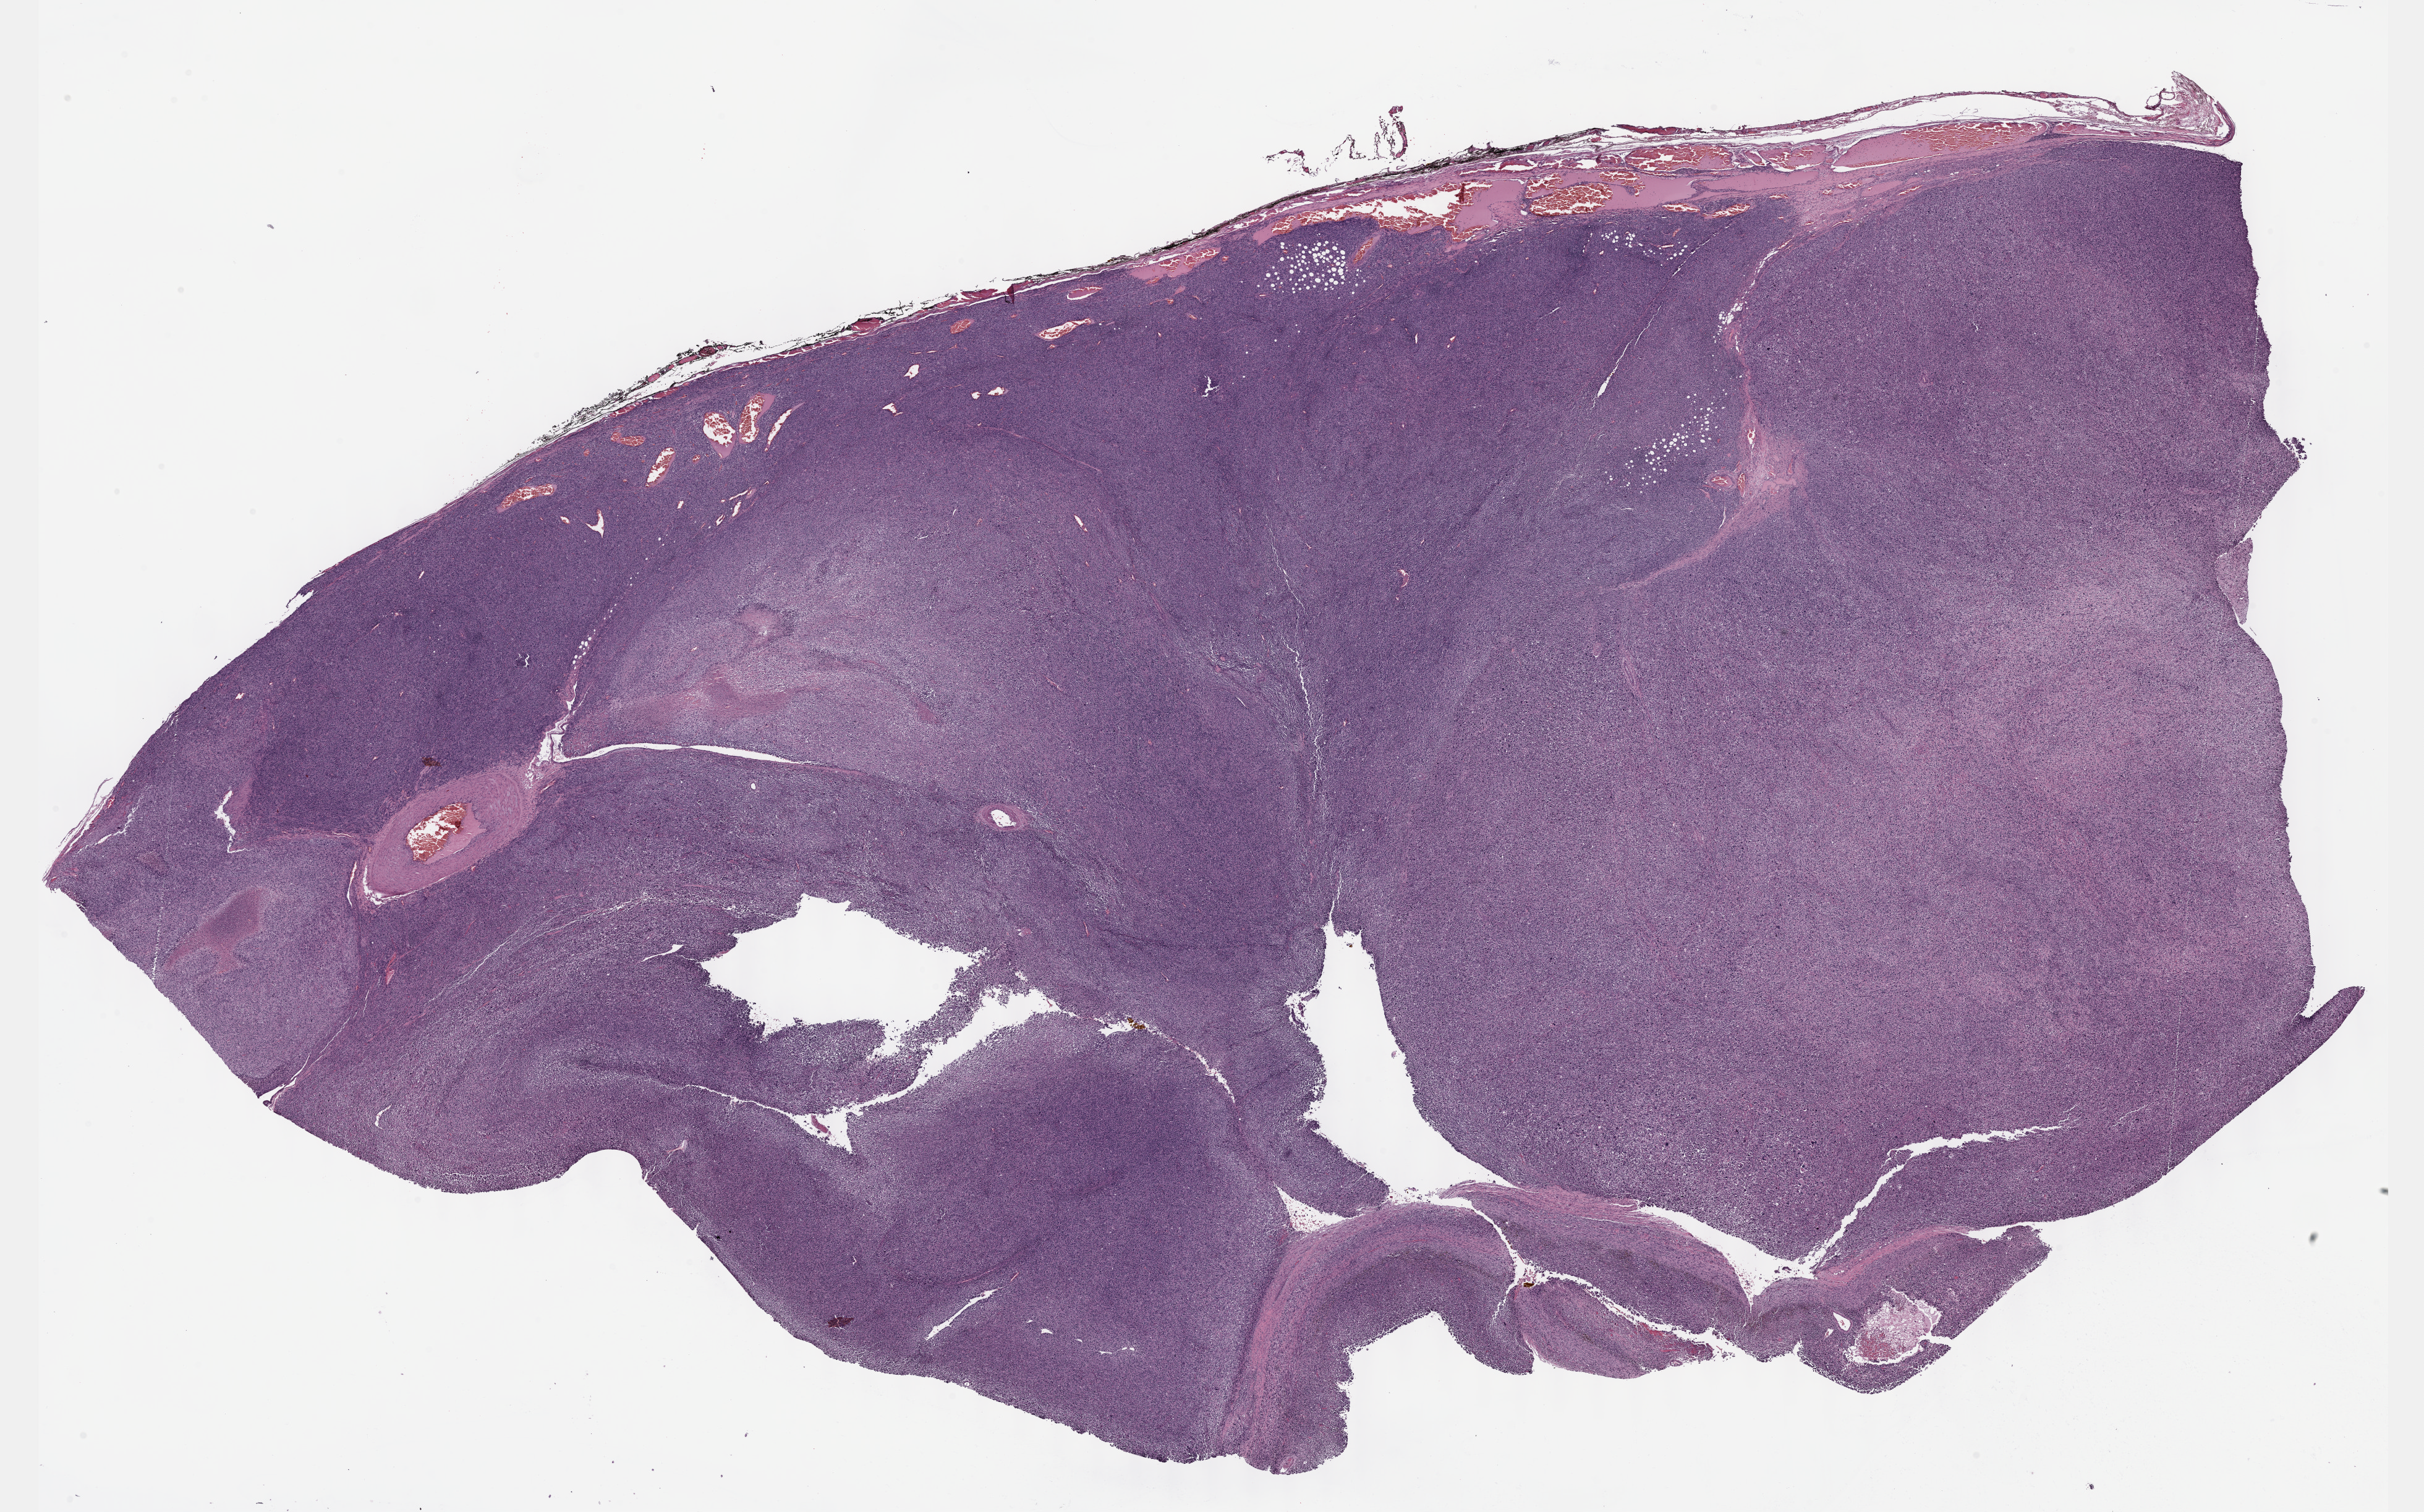
H&E-stained whole-slide image, shown as a low-resolution overview of the whole scanned area (about 31.7 x 19.8 mm, acquisition: 40x scan), formalin-fixed paraffin-embedded (FFPE) diagnostic section, sample: primary tumour, connective, subcutaneous and other soft tissues. Patient: male, age at initial diagnosis 29 years.
Histologic diagnosis: Malignant peripheral nerve sheath tumor.